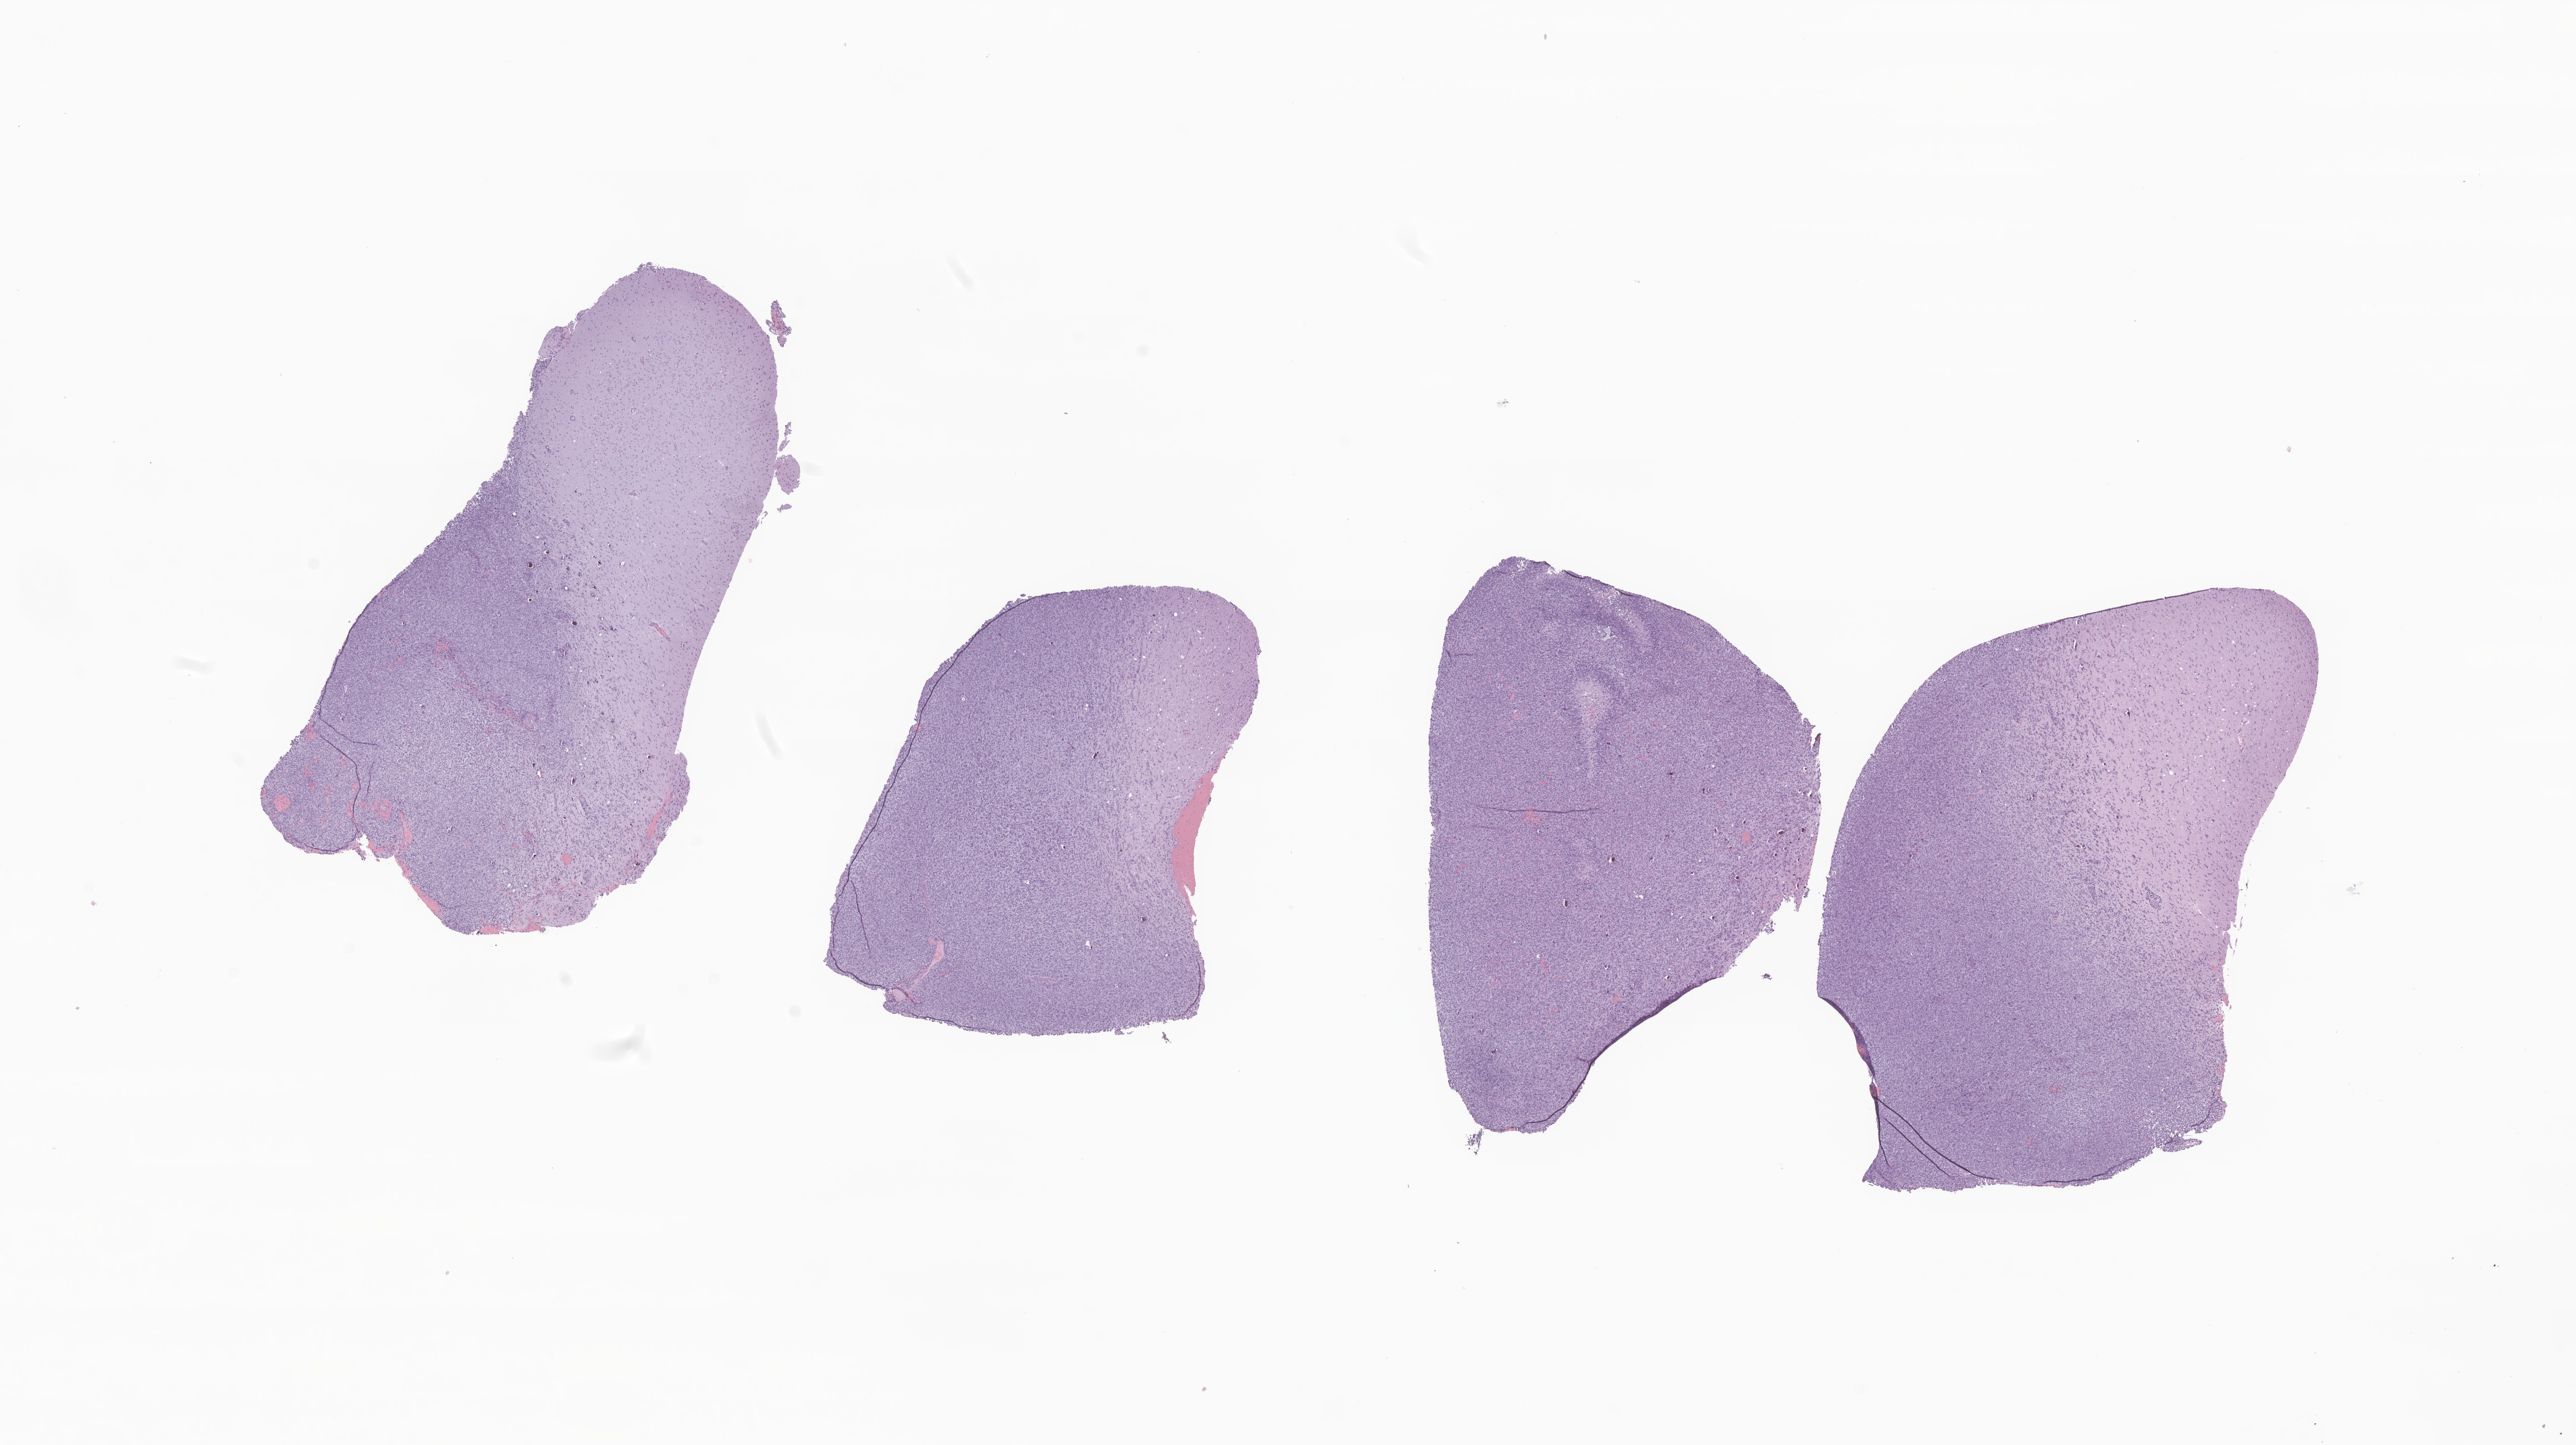
Whole-slide image, hematoxylin and eosin (H&E) stain of tumor tissue from the parietal lobe — low-resolution overview of the scanned area, about 19.4 x 10.9 mm. FFPE section. Patient: male, age 211 months (17 years 7 months).
* diagnosis: Glioma, malignant